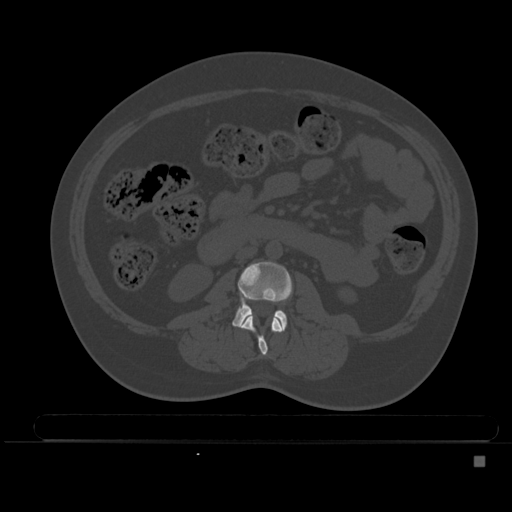
CT including the spine, one axial slice. Position 160 of 495 along the scan axis. Bone window (W 1800 / L 400 HU). 1.5 mm slice thickness. 512 × 512 image matrix, field of view 404 × 404 mm. Female patient, age 33 years. From the clinical record (not read from this slice): primary cancer: breast; vertebrae with lytic lesions (as recorded): T1.
Annotated regions visible in this slice (semi-automatically segmented with operator editing):
- L2 vertebra: box from (x=239, y=315) to (x=283, y=356) px
- L3 vertebra: (x=232, y=261)–(x=292, y=330)